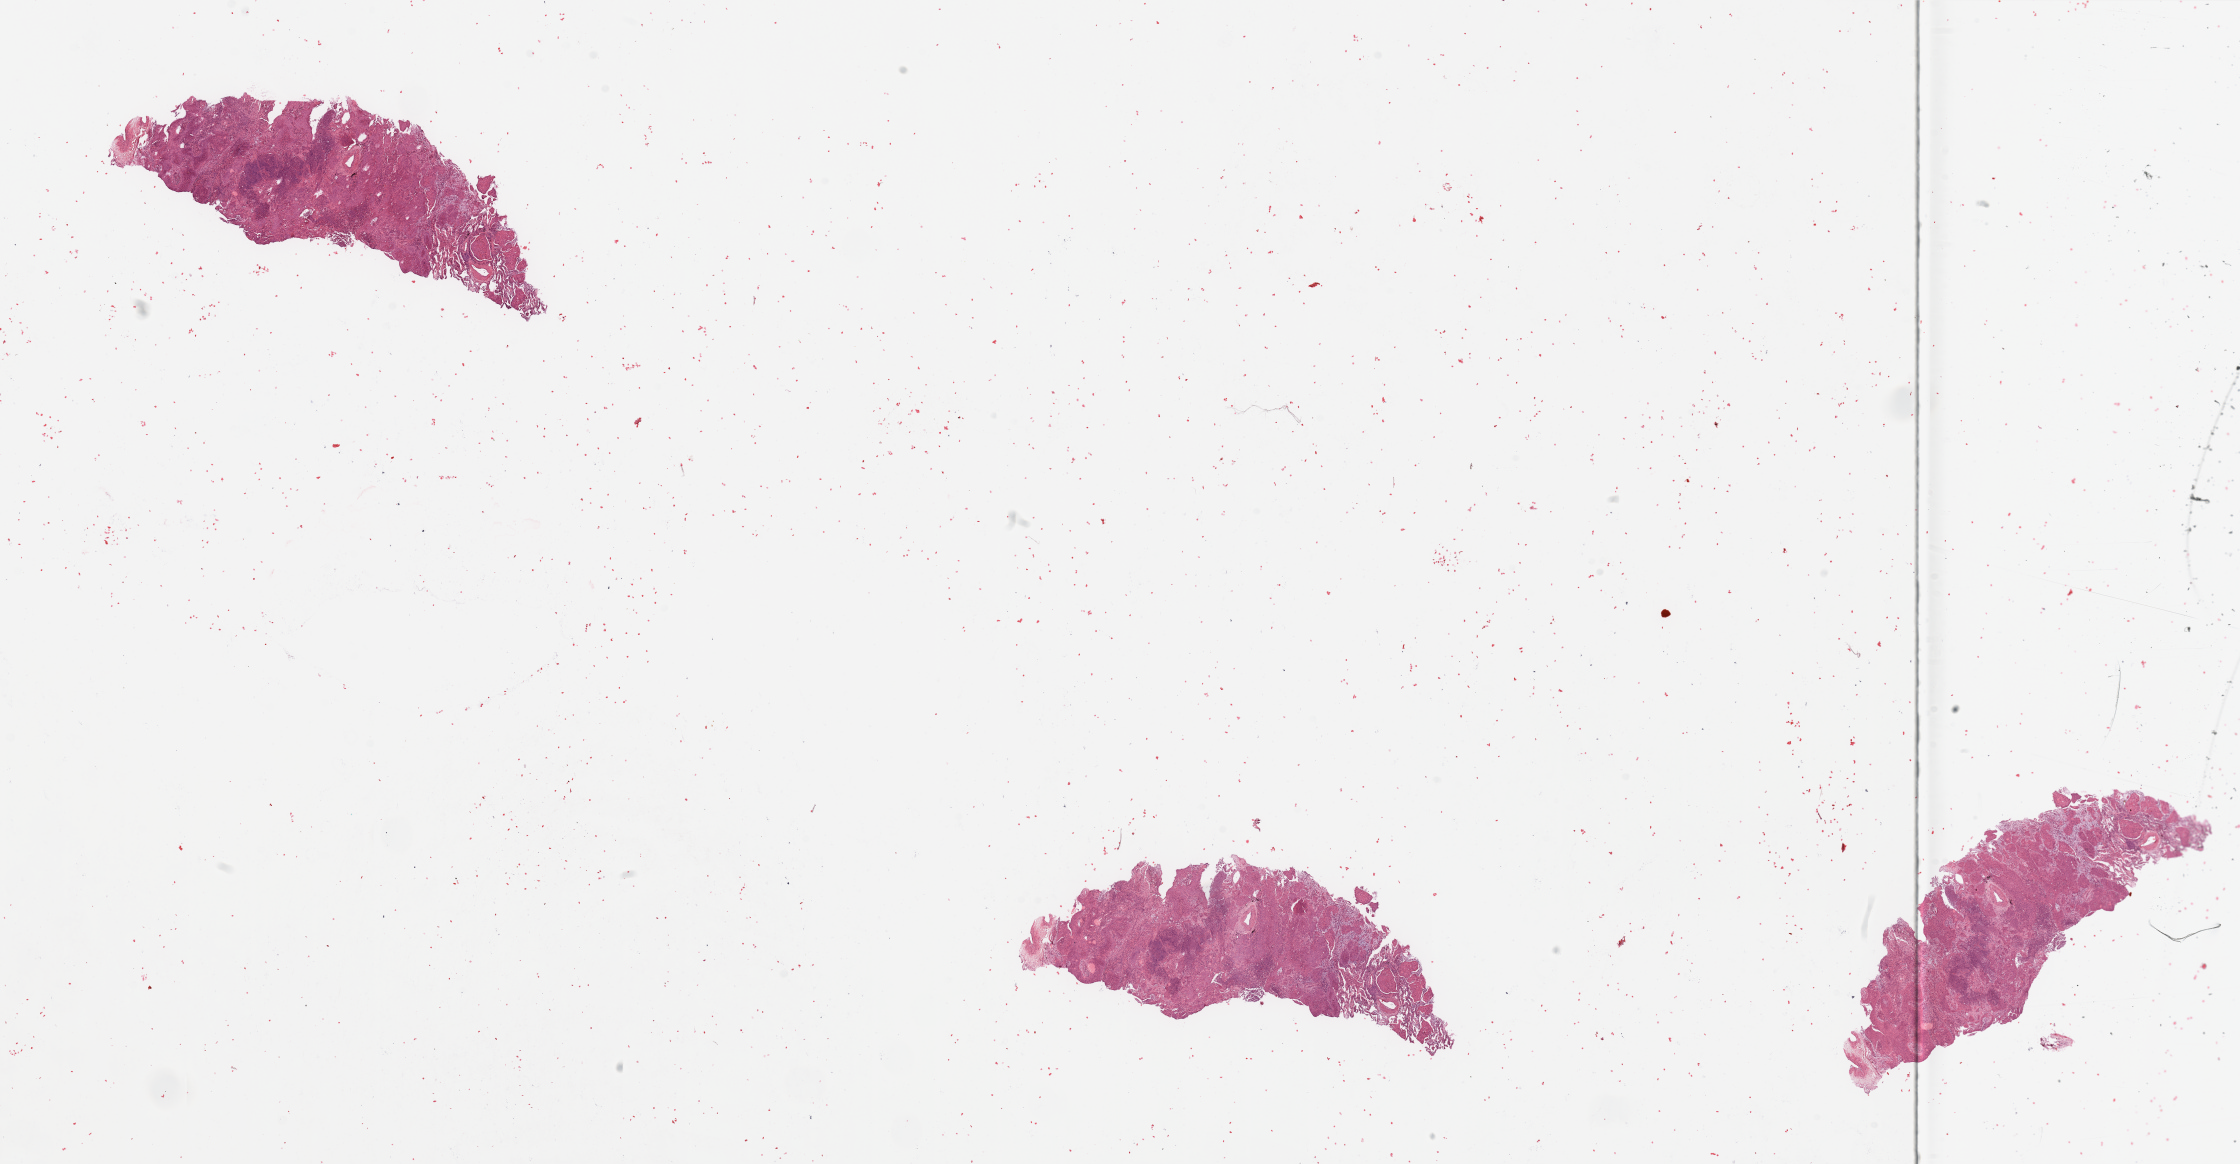
H&E-stained whole-slide image — whole scanned area (about 35.4 x 18.4 mm, slide scanned at 20x) shown as a low-resolution overview, tumour tissue sample, sampled site: lung. 72-year-old female patient. Histologic grade: G2 (moderately differentiated). Slide review estimates, as recorded: tumour nuclei 70%, necrosis 15%.
AJCC pathologic stage: IIB. Diagnosis: Squamous cell carcinoma, NOS. Primary tumour site (as recorded): left lower lobe.